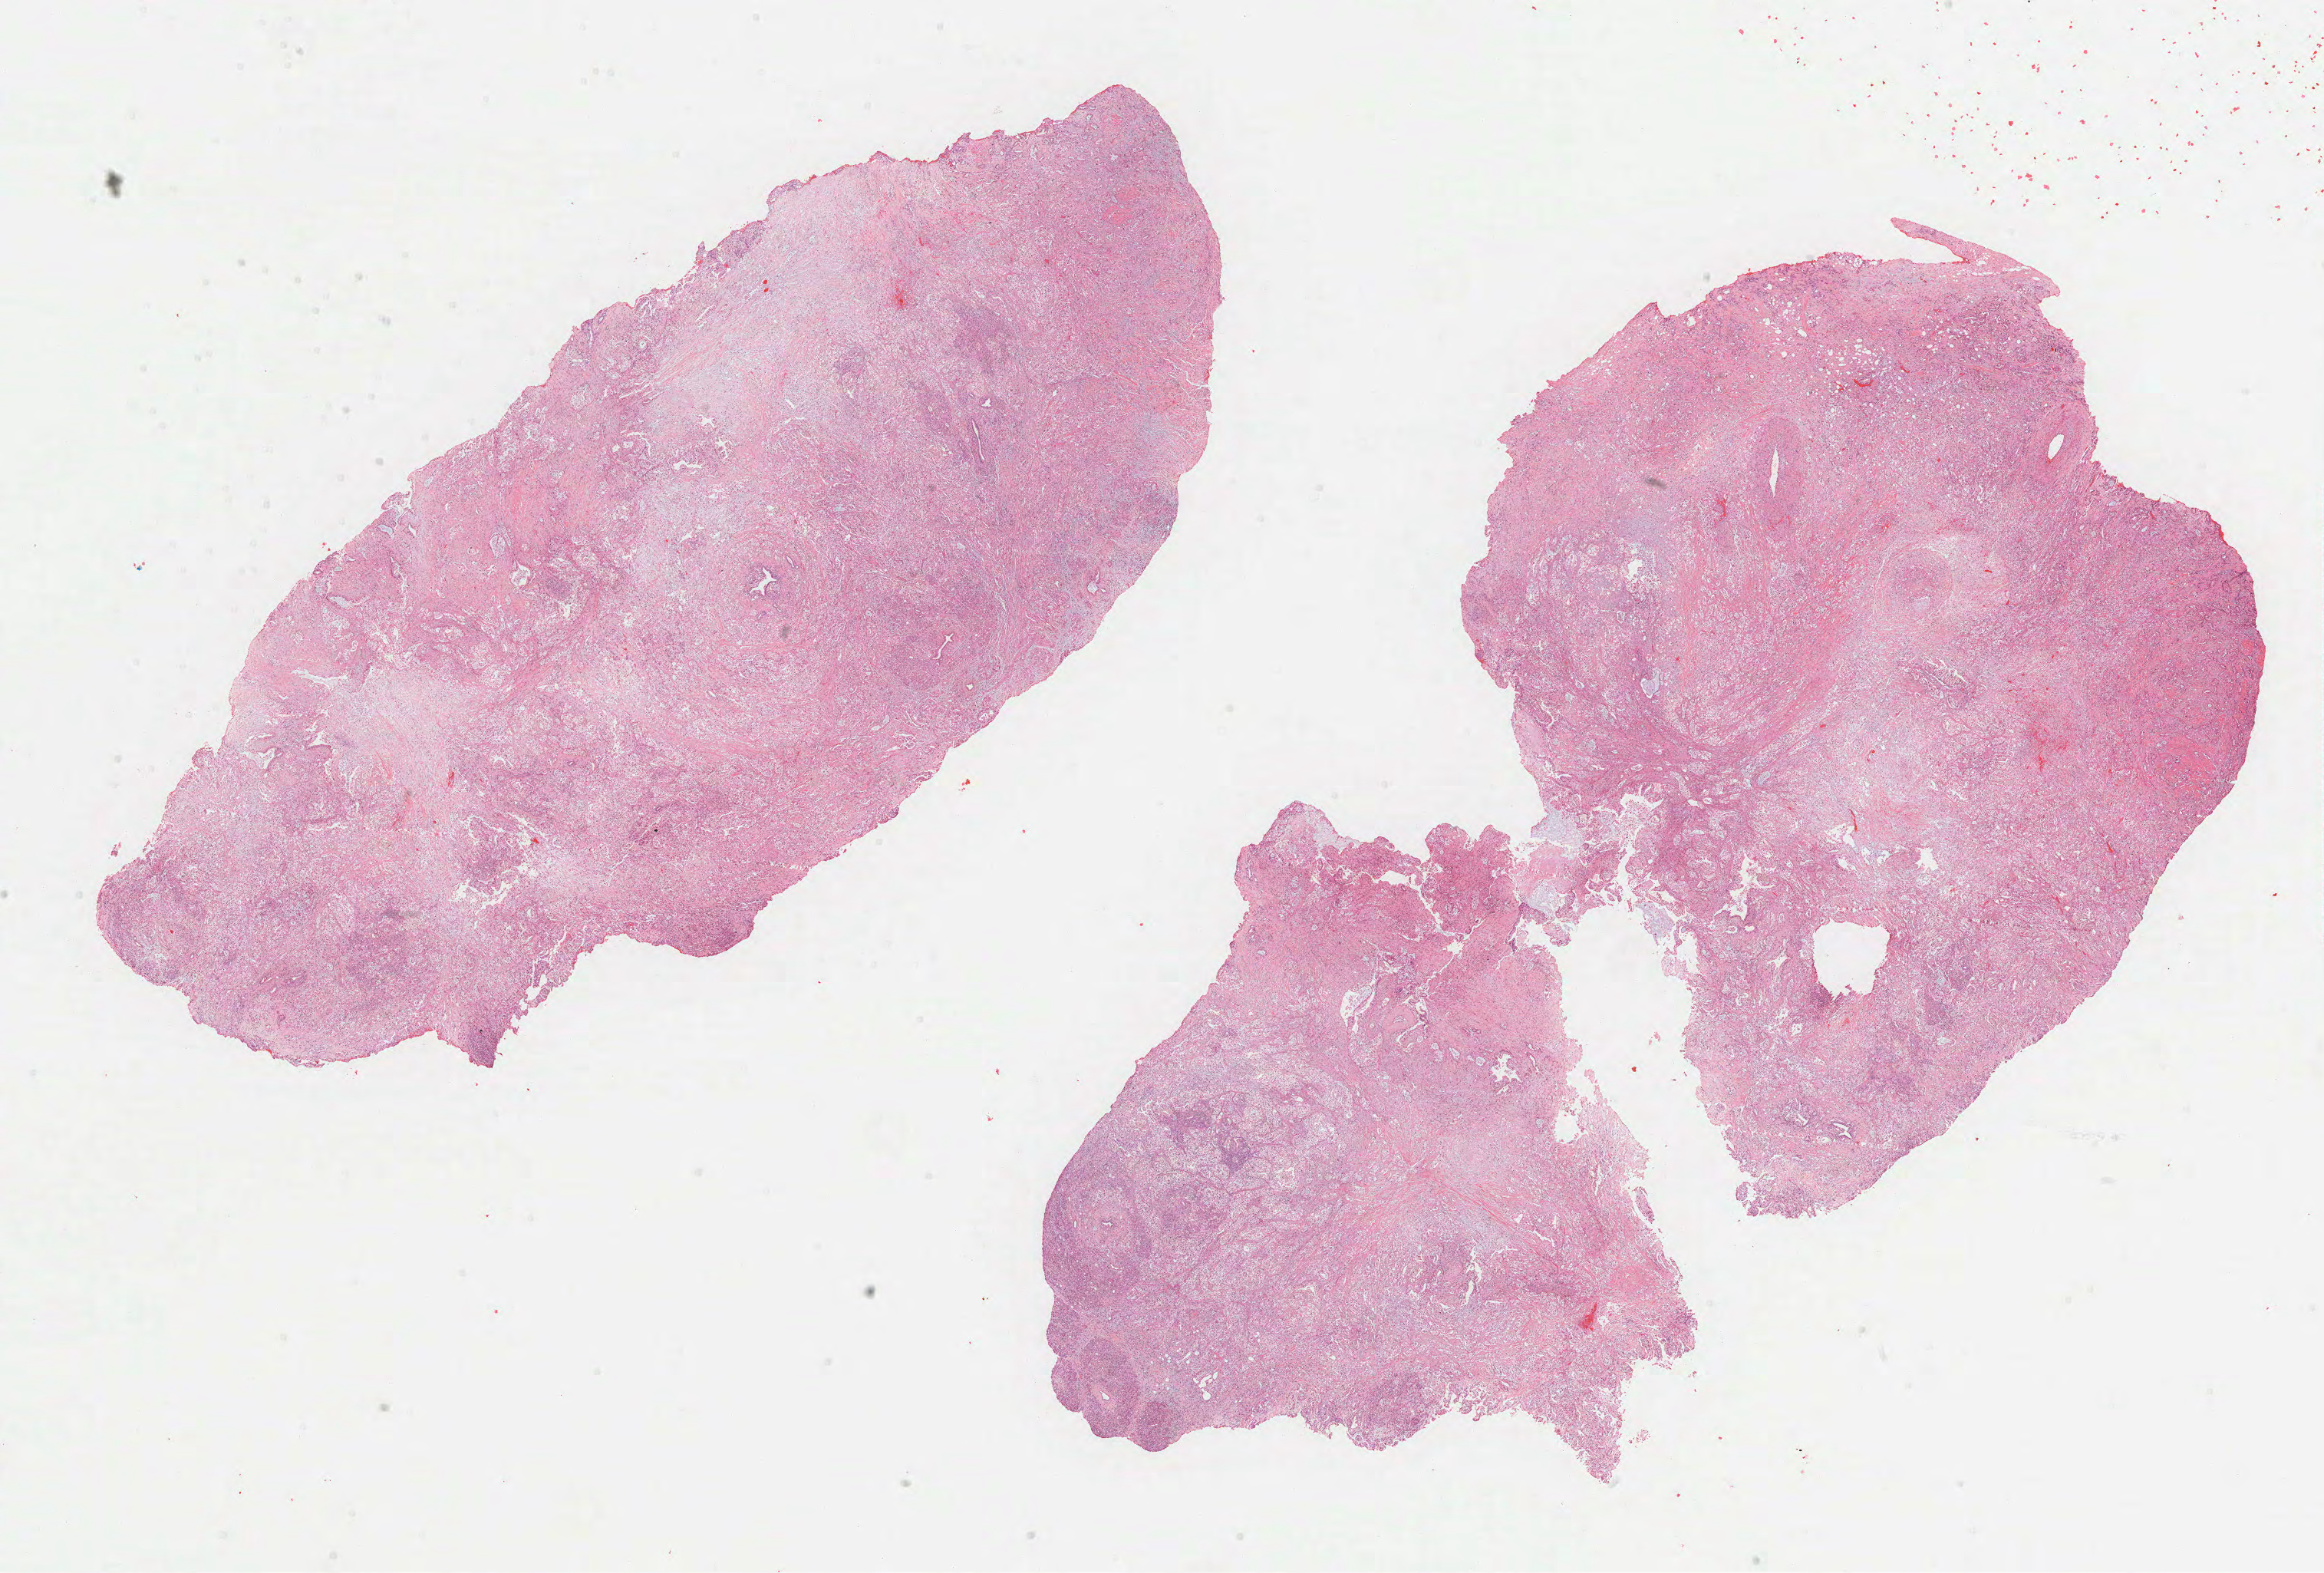
H&E-stained whole-slide image, shown as a low-resolution overview of the whole scanned area (about 24.5 x 16.6 mm, from a 40x scan); formalin-fixed paraffin-embedded (FFPE) diagnostic section; primary tumour sample from the pancreas. Male patient; age at initial diagnosis 65 years. Histologic grade: G3 (poorly differentiated).
Histologic diagnosis: Infiltrating duct carcinoma, NOS (head of pancreas). Lymph nodes positive (case pathology): 2 of 25 examined. AJCC pathologic stage: IIB (7th edition).